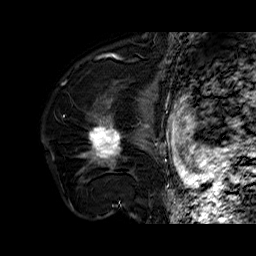
Breast MRI (dynamic contrast-enhanced), one sagittal slice; position 44 of 60 along the scan axis; dynamic contrast-enhanced series, time point 2 of 6 at this slice position (early post-contrast); 1.5 T; TE 6.4 ms, TR 32.7 ms; 4 mm slice thickness; 256 × 256 image matrix, field of view 200 × 200 mm. Female patient. From the clinical record (not read from this slice): setting: breast cancer imaged before/during neoadjuvant chemotherapy; receptor status: HR-positive, HER2-negative.
Outlined on this slice (semi-automatically segmented with operator editing):
- analysis volume of interest (the breast-tissue region the enhancement analysis was run in; not a lesion): bounding box [x1, y1, x2, y2] px = [78, 110, 141, 178]
- tumour enhancement mask (voxels above the 100 % enhancement threshold inside the analysis volume of interest): [90, 120, 121, 163]